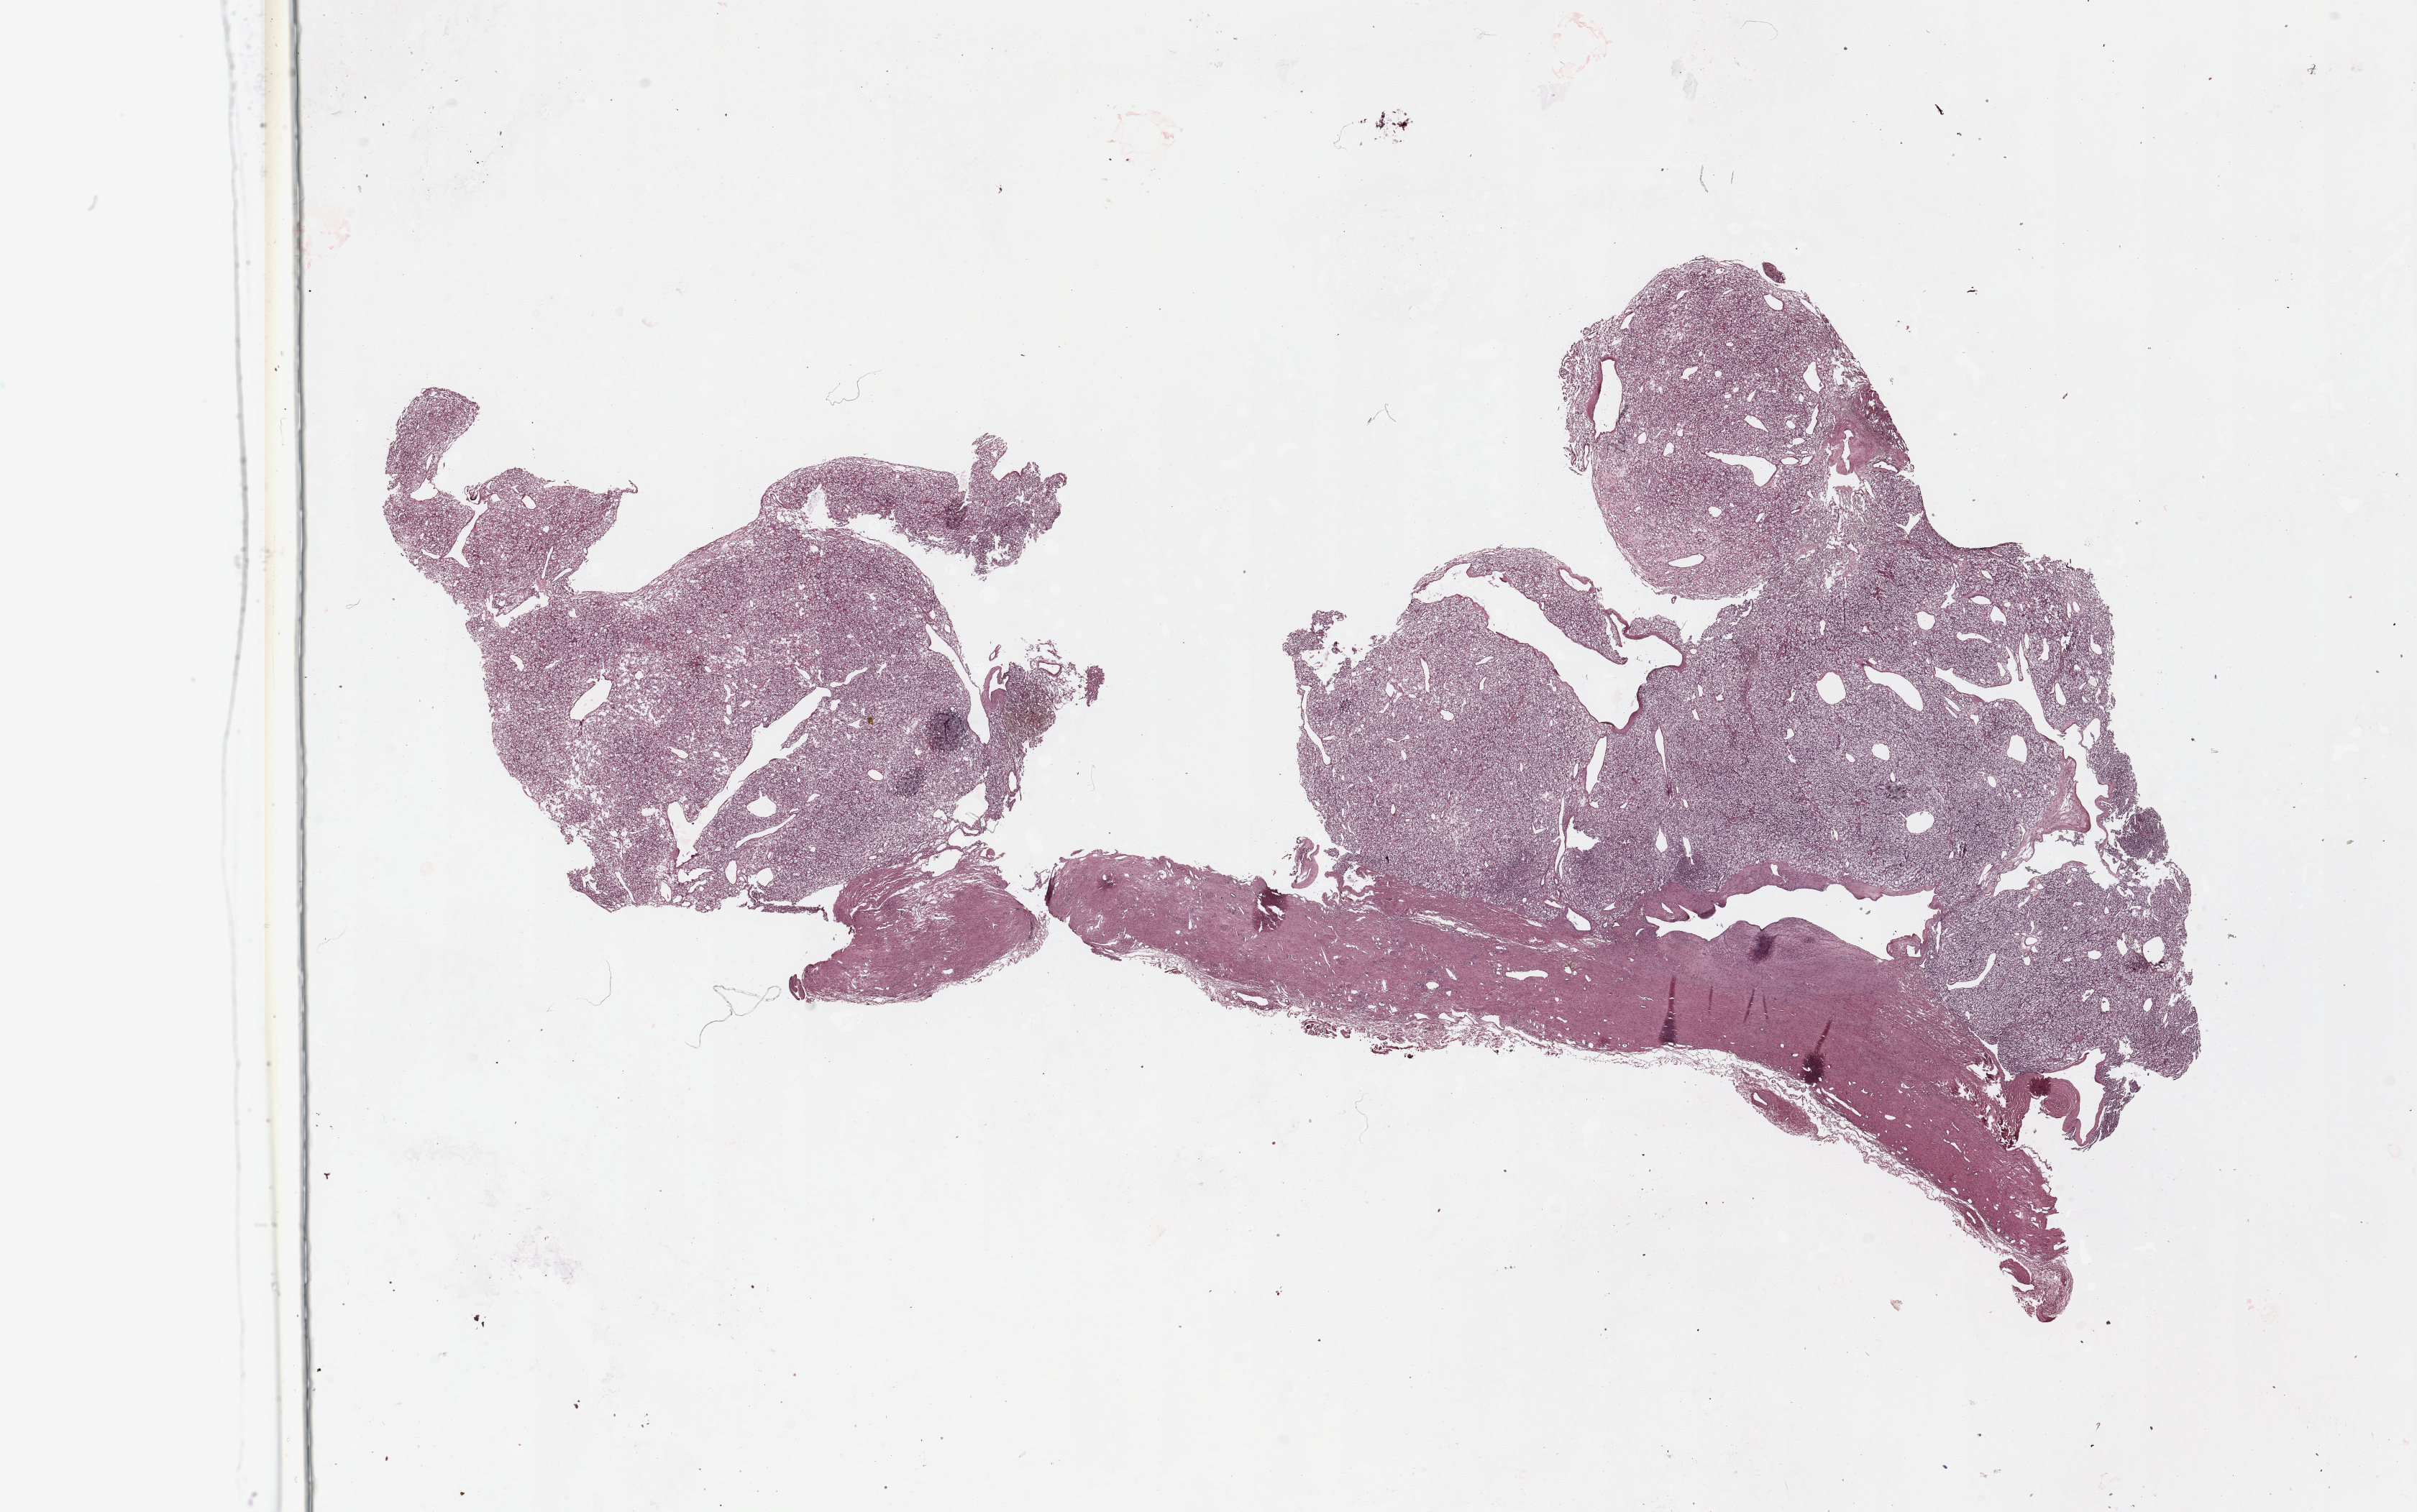
H&E-stained whole-slide image, shown as a low-resolution overview of the whole scanned area (about 26.6 x 16.6 mm, from a 20x scan); tumour tissue sample, sampled site: kidney. Patient: male, age 67 years. Histologic grade: G1 (well differentiated). Slide review estimates, as recorded: tumour nuclei 90%, necrosis 5%.
Histologic diagnosis: Renal cell carcinoma, NOS. Primary tumour site (as recorded): upper pole. AJCC pathologic stage: I.